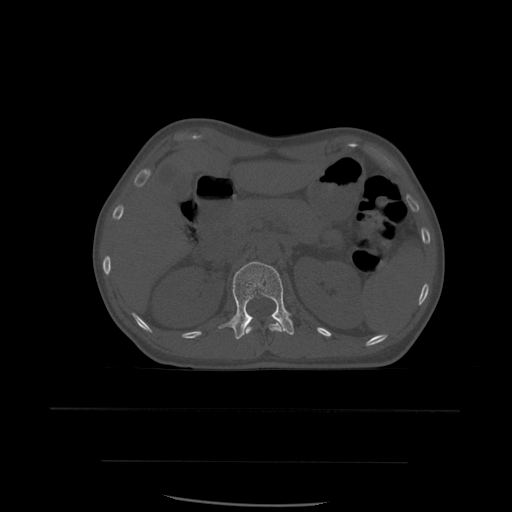
CT including the spine, one axial slice; position 255 of 574 along the scan axis; bone window (W 1800 / L 400 HU); 512 × 512 image matrix. Patient age 48 years. Case-level facts recorded for this patient, not image findings: primary cancer: lung.
Annotated regions visible in this slice (semi-automatic segmentation, software-assisted and operator-edited):
- L1 vertebra: bounding box (x1, y1, x2, y2) in pixels: (219, 262, 295, 340)
- T12 vertebra: (246, 319, 284, 334)